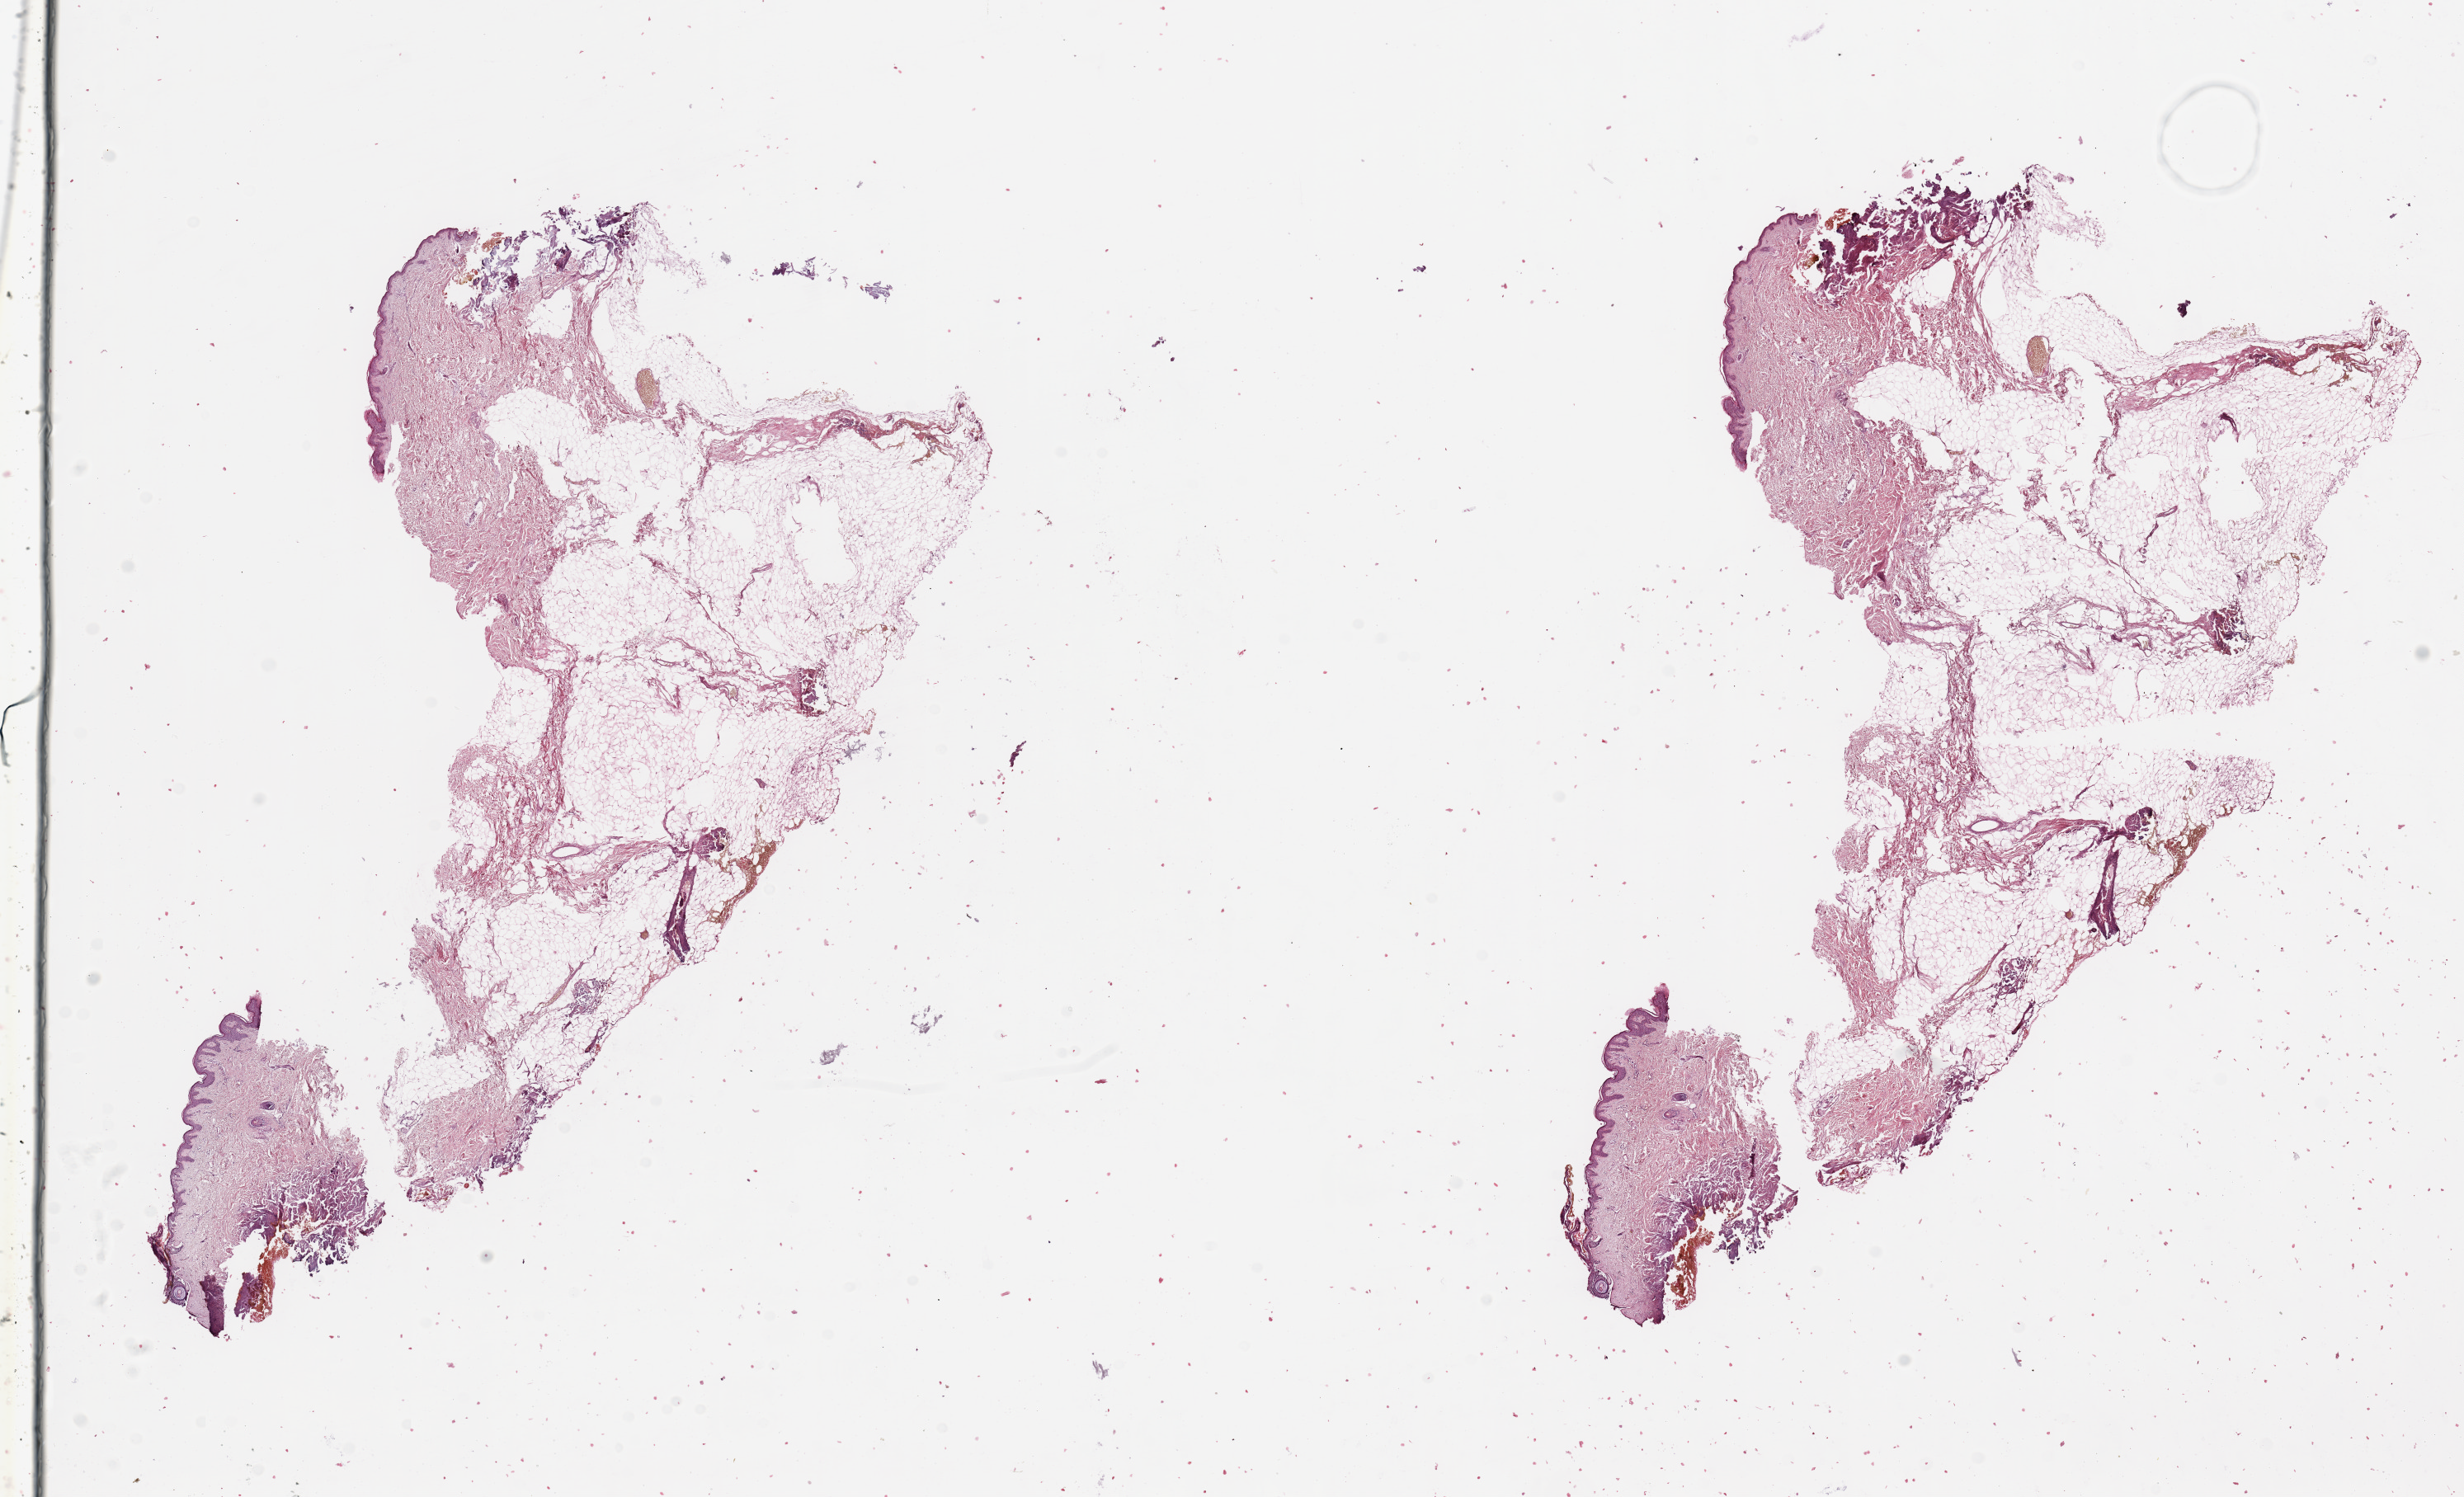
Digitized H&E tissue section (whole slide), low-resolution overview of the scanned area, about 23.6 x 14.4 mm. Normal (non-tumour) tissue sample, sampled site: trunk. Female, 54 y/o.
* this section: normal (non-tumour) tissue from the same patient
* patient diagnosis: Malignant melanoma, NOS